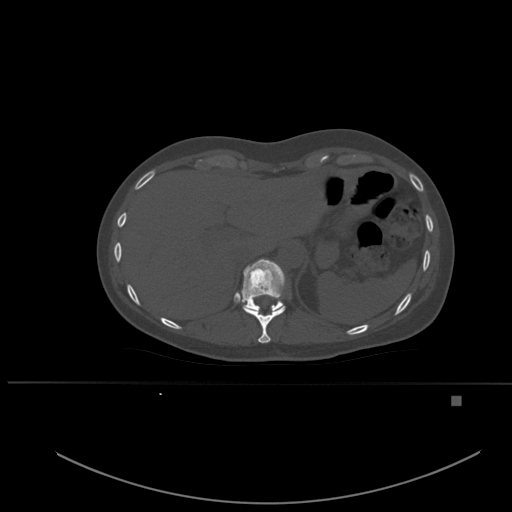
CT including the spine, one axial slice. Position 281 of 651 along the scan axis. Bone window (W 1800 / L 400 HU). 1.5 mm slice thickness. 512 × 512 image matrix. Patient: female, 49 years. Case-level facts recorded for this patient, not image findings: primary cancer: breast; vertebrae with lytic lesions (as recorded): L3, T12, L4.
Structures marked on this image (semi-automatic segmentation, software-assisted and operator-edited):
- T10 vertebra: box from (x=243, y=306) to (x=286, y=343) px
- T11 vertebra: (x=241, y=259)–(x=286, y=312)